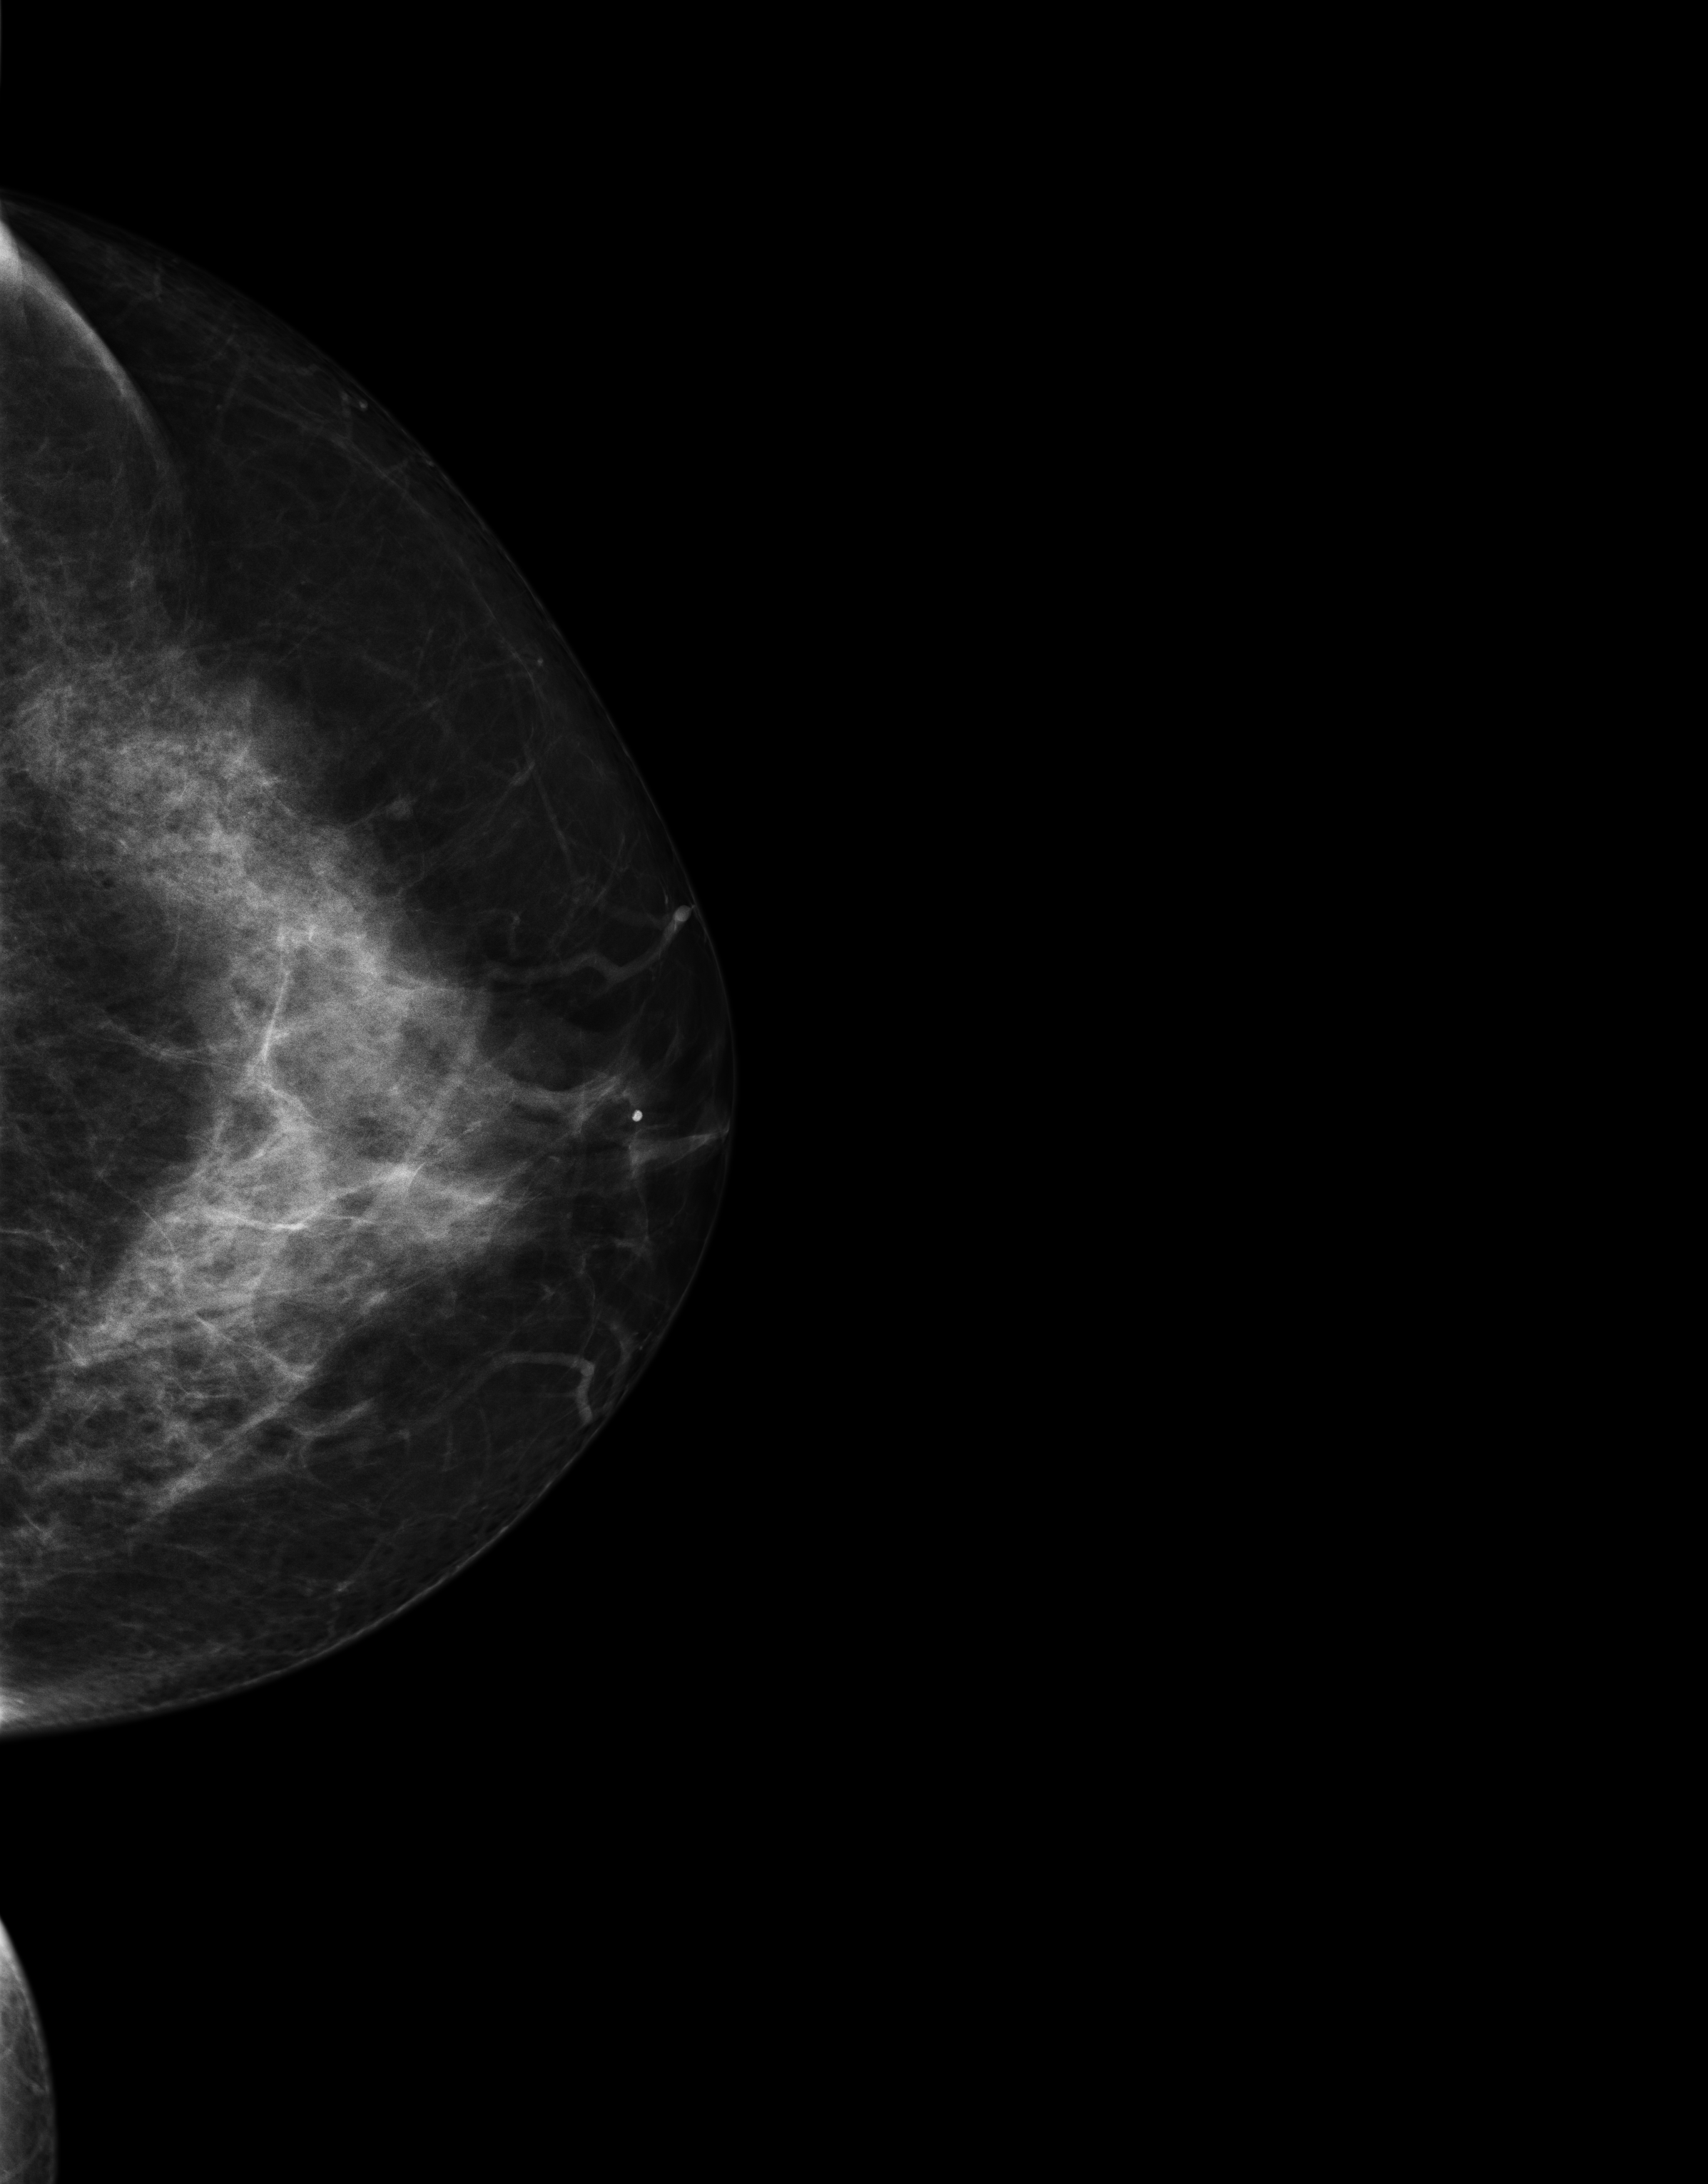
Digital mammogram (FFDM), left breast, craniocaudal (CC) view, screening examination, compressed breast thickness 79 mm, system: Senographe Essential ADS_56.21.3. Female patient, age 47 years.
Breast density at the screening exam (both breasts): heterogeneously dense (BI-RADS density category c). Final BI-RADS assessment for this screening round (tomosynthesis exam, both breasts): category 1. Recall: no recall after this screen.